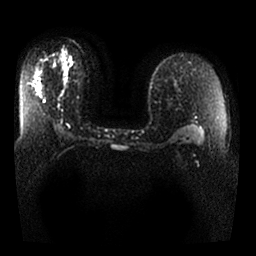
Breast MRI, one axial slice. Position 15 of 25 along the scan axis. Diffusion-weighted series; image 2 of 4 stored at this slice position (different b-values; order by instance number). 1.5 T. 256 × 256 image matrix, field of view 340 × 340 mm. Female patient.
Outlined on this slice (manually delineated by an expert):
- tumour on diffusion-weighted imaging: box from (x=62, y=55) to (x=68, y=72) px